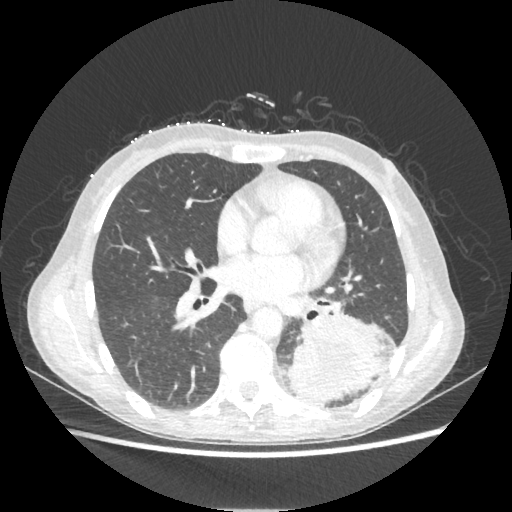
Chest CT, one axial slice; reconstruction kernel STANDARD; 80 kVp; lung window (W 1500 / L -600 HU); 1.25 mm slice thickness; 512 × 512 image matrix, field of view 360 × 360 mm. Patient: female, 53 years. Case-level facts recorded for this patient, not image findings: clinical TNM (as recorded): T3 N0 M0.
Outlined on this slice (bounding box drawn by a radiologist):
- lung tumour (recorded histology: adenocarcinoma): box from (x=290, y=313) to (x=387, y=403) px